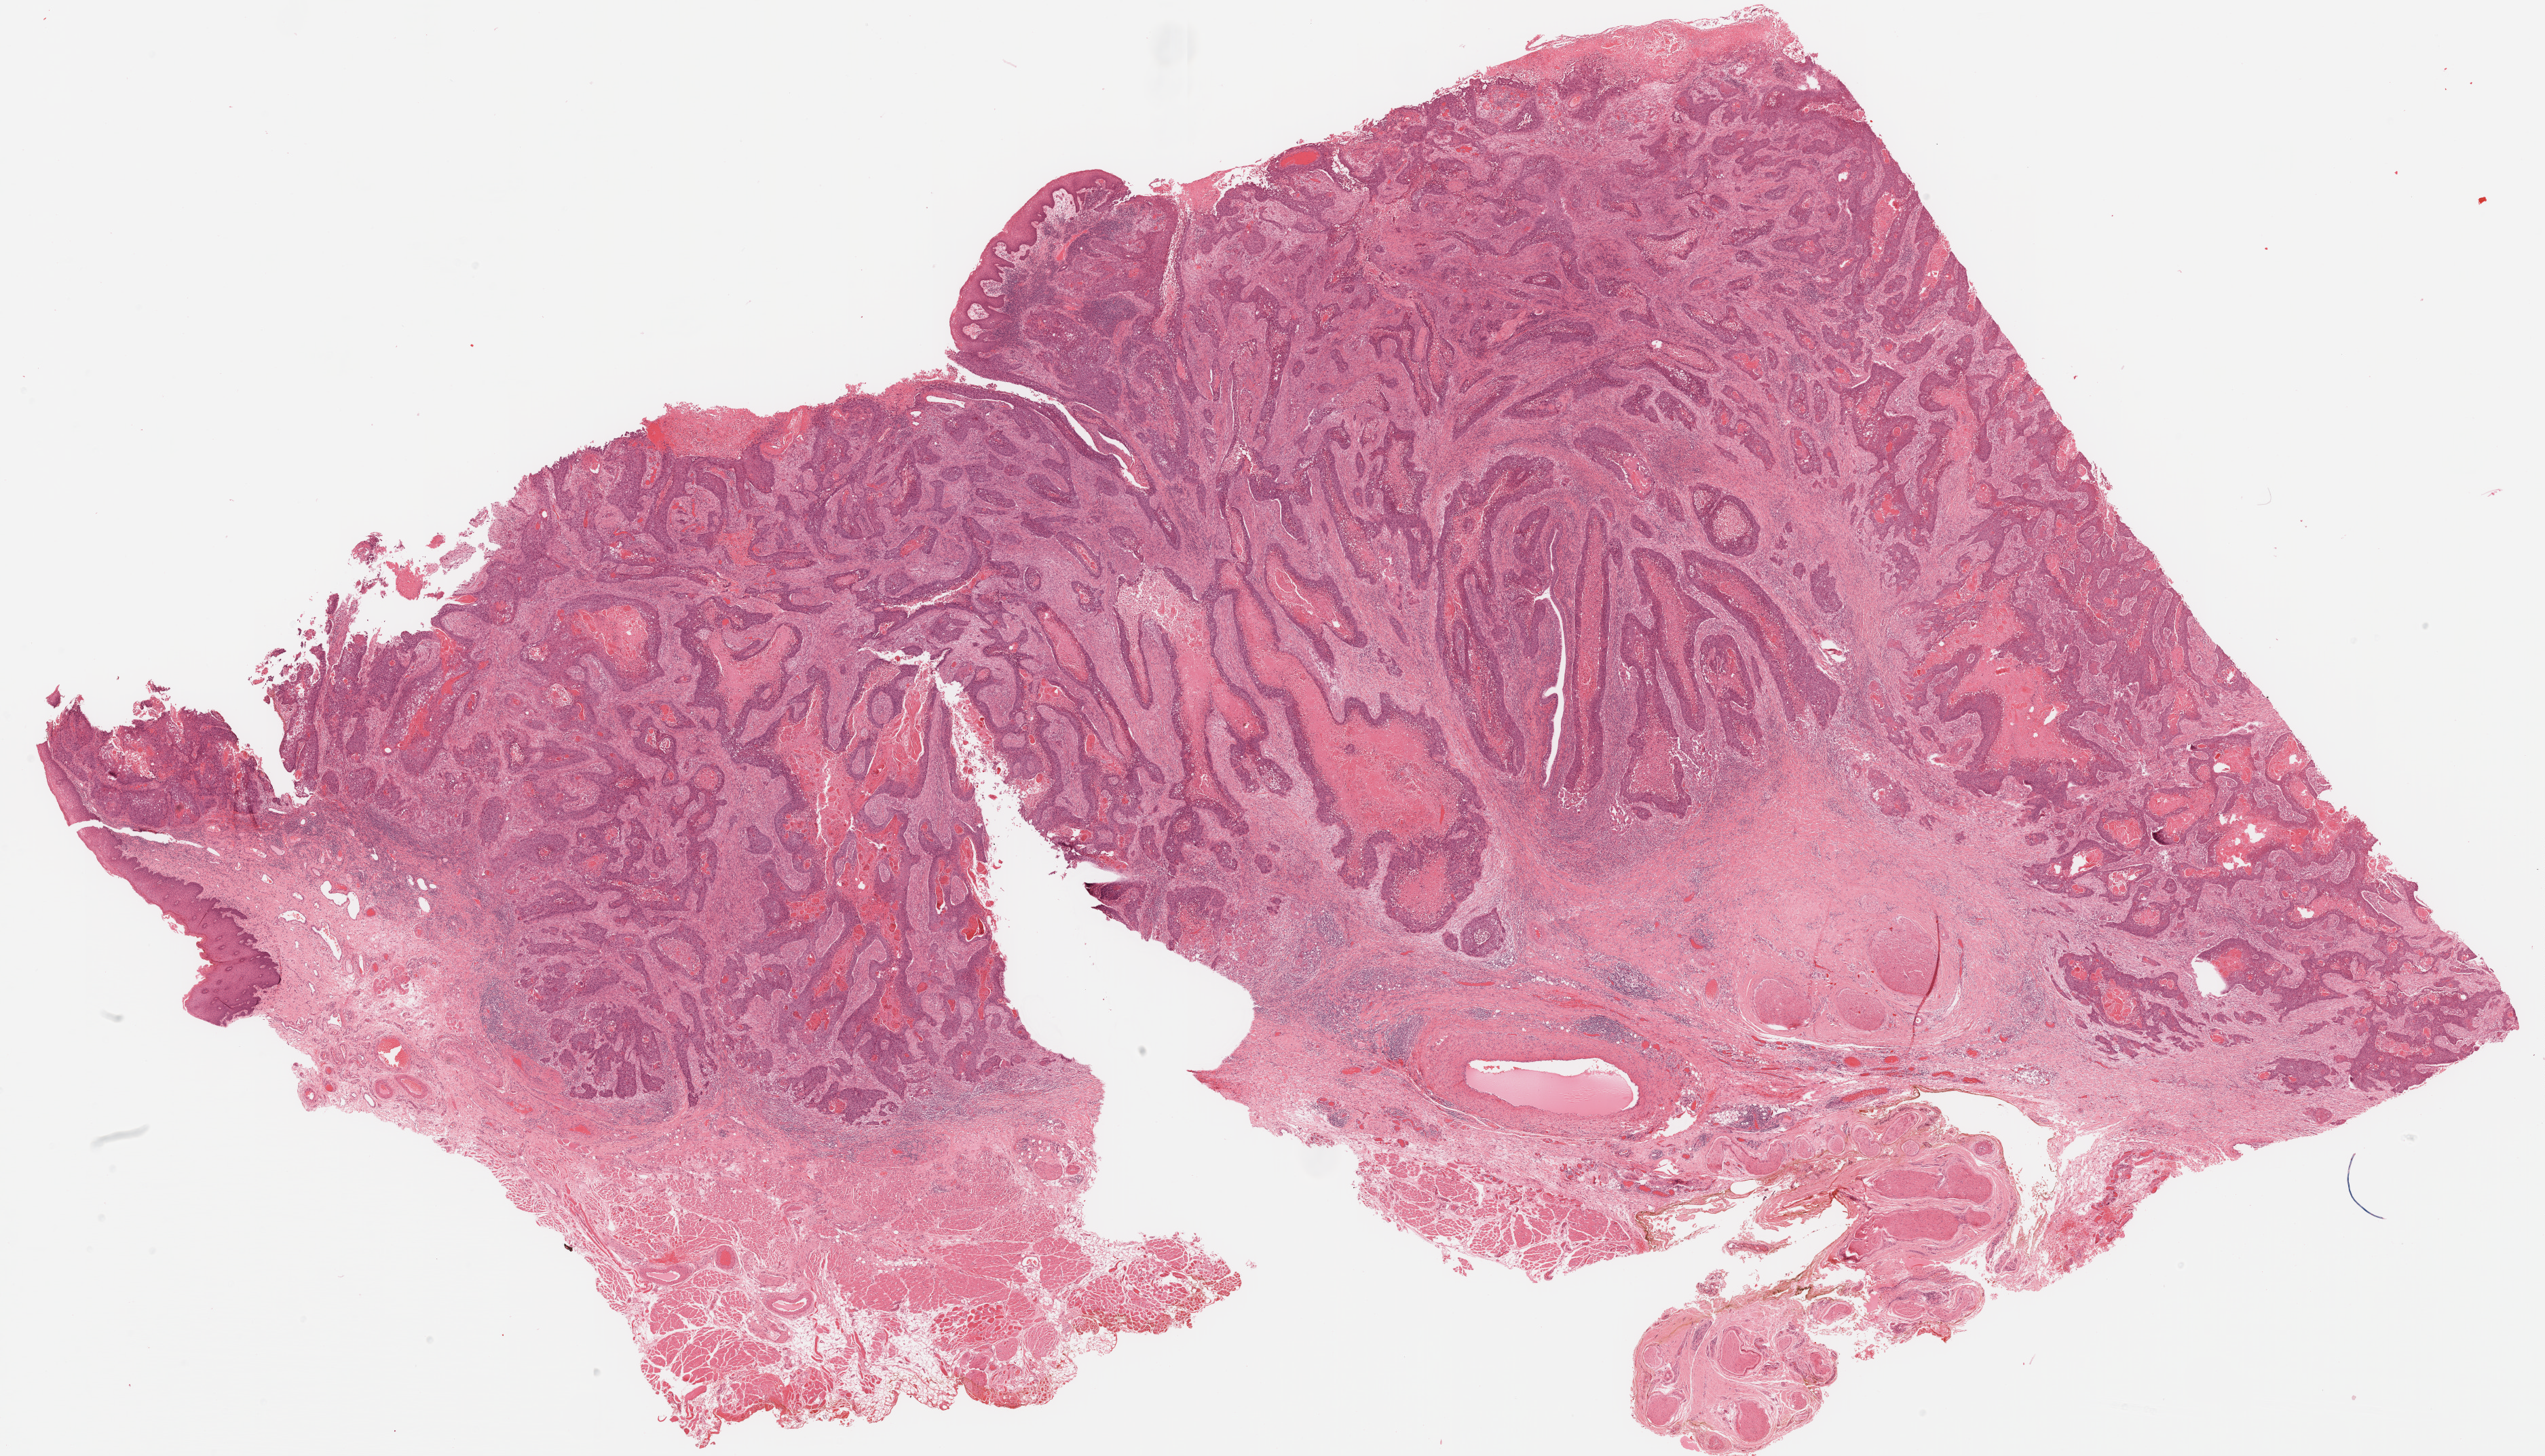
H&E-stained whole-slide image — a low-resolution overview of the entire scanned area, about 30.1 x 17.2 mm (slide scanned at 20x). Formalin-fixed paraffin-embedded (FFPE) diagnostic section. Primary tumour sample from the head and neck. Male patient; age at initial diagnosis 87 years. Histologic grade: G2 (moderately differentiated).
Lymph nodes positive (case pathology): 0 of 31 examined. Laterality: left. AJCC pathologic stage: III (6th edition). Diagnosis: Squamous cell carcinoma, NOS.